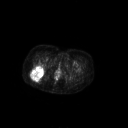
FDG PET of an extremity soft-tissue mass (from a PET/CT study), one axial slice. Position 53 of 267 along the scan axis. 3.27 mm slice thickness. 128 × 128 image matrix, field of view 700 × 700 mm. Female patient, age 70 years. From the clinical record (not read from this slice): histological type: synovial sarcoma; grade: intermediate; site of the primary tumour: right buttock.
Outlined on this slice (expert contour drawn on MRI and transferred to this co-registered scan by the dataset authors):
- gross tumour volume including surrounding oedema: bounding box <30,64,45,81> (left, top, right, bottom; pixels)
- gross tumour volume (mass): <30,64,45,81>